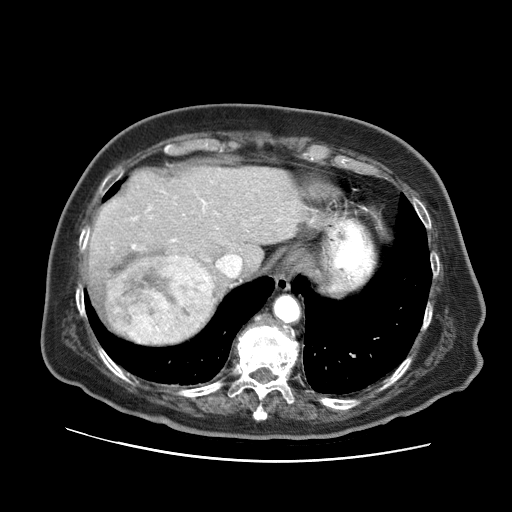
Contrast-enhanced abdominal CT (liver protocol), one axial slice. Slice 54 of 73 in the series (ordered by position). Reconstruction kernel STANDARD. Soft-tissue window (W 400 / L 40 HU). 512 × 512 image matrix, field of view 380 × 380 mm. Case-level facts recorded for this patient, not image findings: diagnosis: hepatocellular carcinoma (patient treated with transarterial chemoembolisation; whether this scan precedes or follows treatment is not stated here); TNM stage (as recorded): Stage-I; Child-Pugh class: A; tumour differentiation: well differentiated.
Outlined on this slice (semi-automatic segmentation, software-assisted and operator-edited):
- liver parenchyma outside the tumour (the mass and vessels are separate outlines, so this box may not span the whole liver): bounding box (x1, y1, x2, y2) in pixels: (88, 166, 306, 346)
- mass: (104, 246, 215, 344)
- liver vessels: (132, 200, 207, 249)